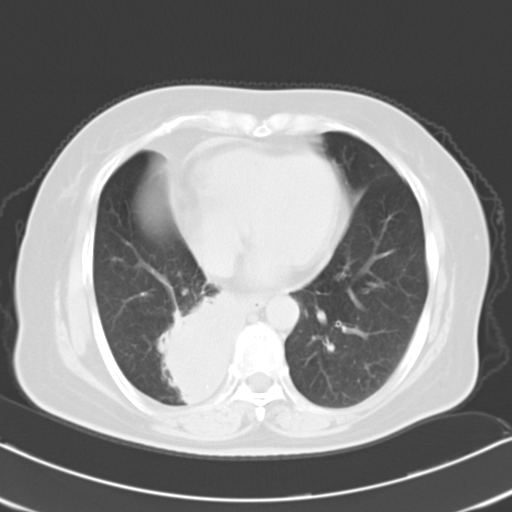
Chest CT, one axial slice. Slice 7 of 21 in the series (ordered by position). Reconstruction kernel B40f. Lung window (W 1500 / L -600 HU). 10 mm slice thickness. 512 × 512 image matrix. Female patient, age 61 years. From the clinical record (not read from this slice): clinical TNM (as recorded): T1b N0 M1b.
Structures marked on this image (bounding box drawn by a radiologist):
- lung tumour (recorded histology: squamous cell carcinoma): bounding box <166,284,249,407> (left, top, right, bottom; pixels)